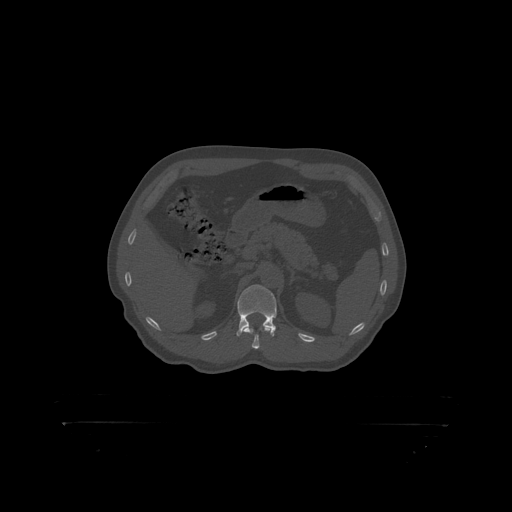
CT including the spine, one axial slice; slice 336 of 399 in the series (ordered by position); 120 kVp; bone window (W 1800 / L 400 HU); 1.25 mm slice thickness; 512 × 512 image matrix, field of view 650 × 650 mm. Male patient, age 46 years. From the clinical record (not read from this slice): primary cancer: skin.
Annotated regions visible in this slice (semi-automatic segmentation, software-assisted and operator-edited):
- L1 vertebra: bounding box <238,285,277,319> (left, top, right, bottom; pixels)